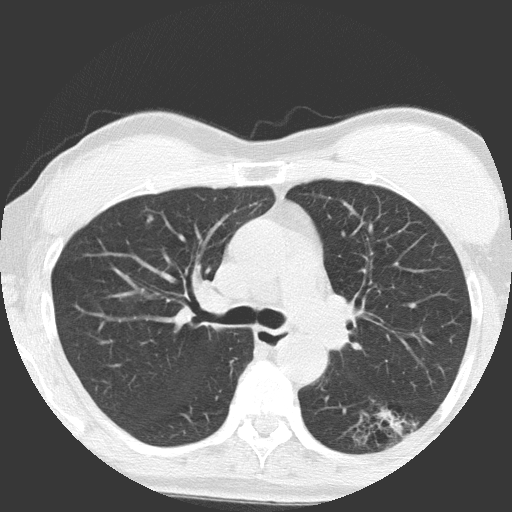
Low-dose screening chest CT, axial slice. First (baseline) screen. Lung window (W 1500 / L -600 HU). 2 mm slice thickness. Lung (sharp) reconstruction kernel (FC51). 120 kVp. Slice 54 of 149 in the series. Female participant, aged 64 years at enrolment.
Expert-annotated lung lesion, box from (x=338, y=392) to (x=425, y=463) px. Screening reader's record for this exam (one nodule recorded; not confirmed to be the boxed lesion): non-calcified nodule or mass ≥4 mm, right upper lobe, 4 × 4 mm, poorly defined margins, ground glass attenuation. Note: the box lies in the patient's left hemithorax on this image, whereas the reader's record names the right lung; they may be different findings.